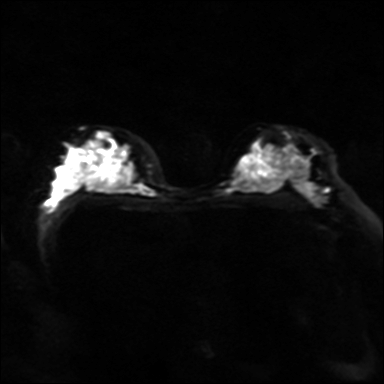
Breast MRI, one axial slice; slice 24 of 40 in the series (ordered by position); diffusion-weighted series; image 2 of 4 stored at this slice position (different b-values; order by instance number); 3 T; 4 mm slice thickness; 384 × 384 image matrix, field of view 320 × 320 mm. Female patient.
Outlined on this slice (manually delineated by an expert):
- tumour on diffusion-weighted imaging: bounding box (x1, y1, x2, y2) in pixels: (97, 132, 108, 137)